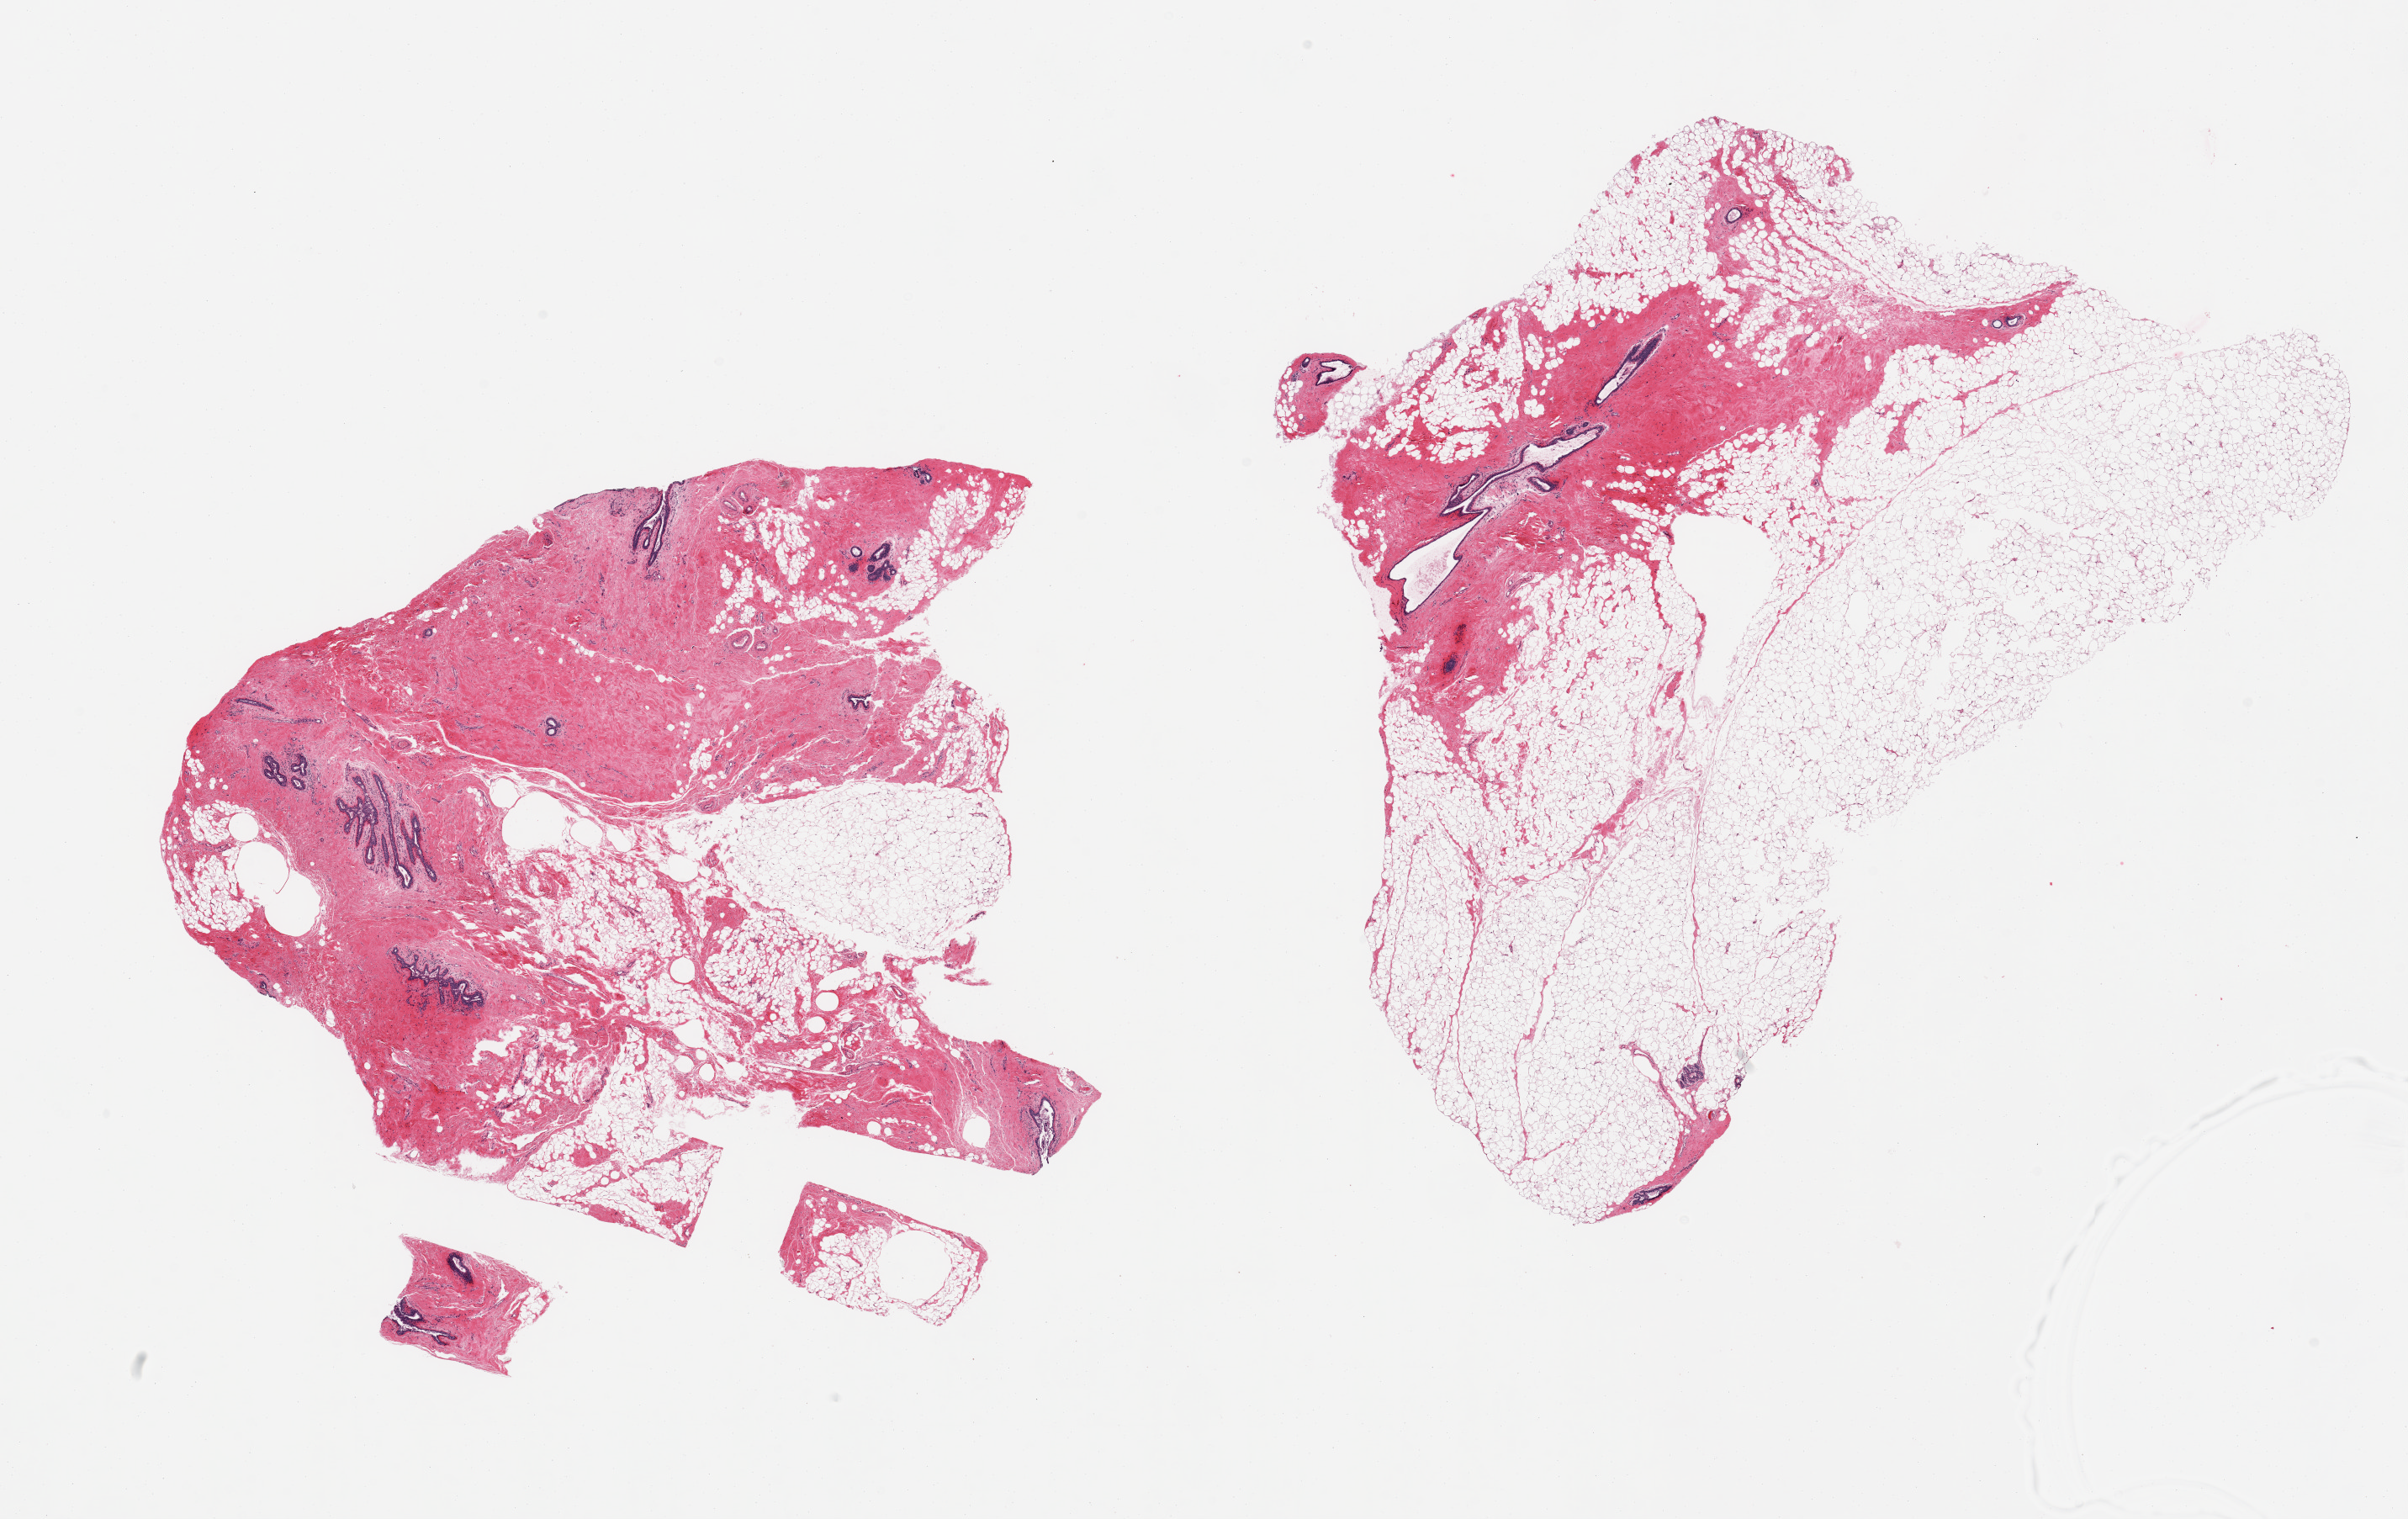
Digitized H&E-stained section, brightfield — a low-resolution overview of the entire scanned area, about 22.6 x 14.3 mm (slide scanned at 20x), PAXgene-fixed paraffin-embedded (PFPE) section, target tissue: breast, tissue donor sample. Female donor.
Pathologist's review note for this sample: 2 pieces, ductal/lobular elements, with typical post menopausal regression.